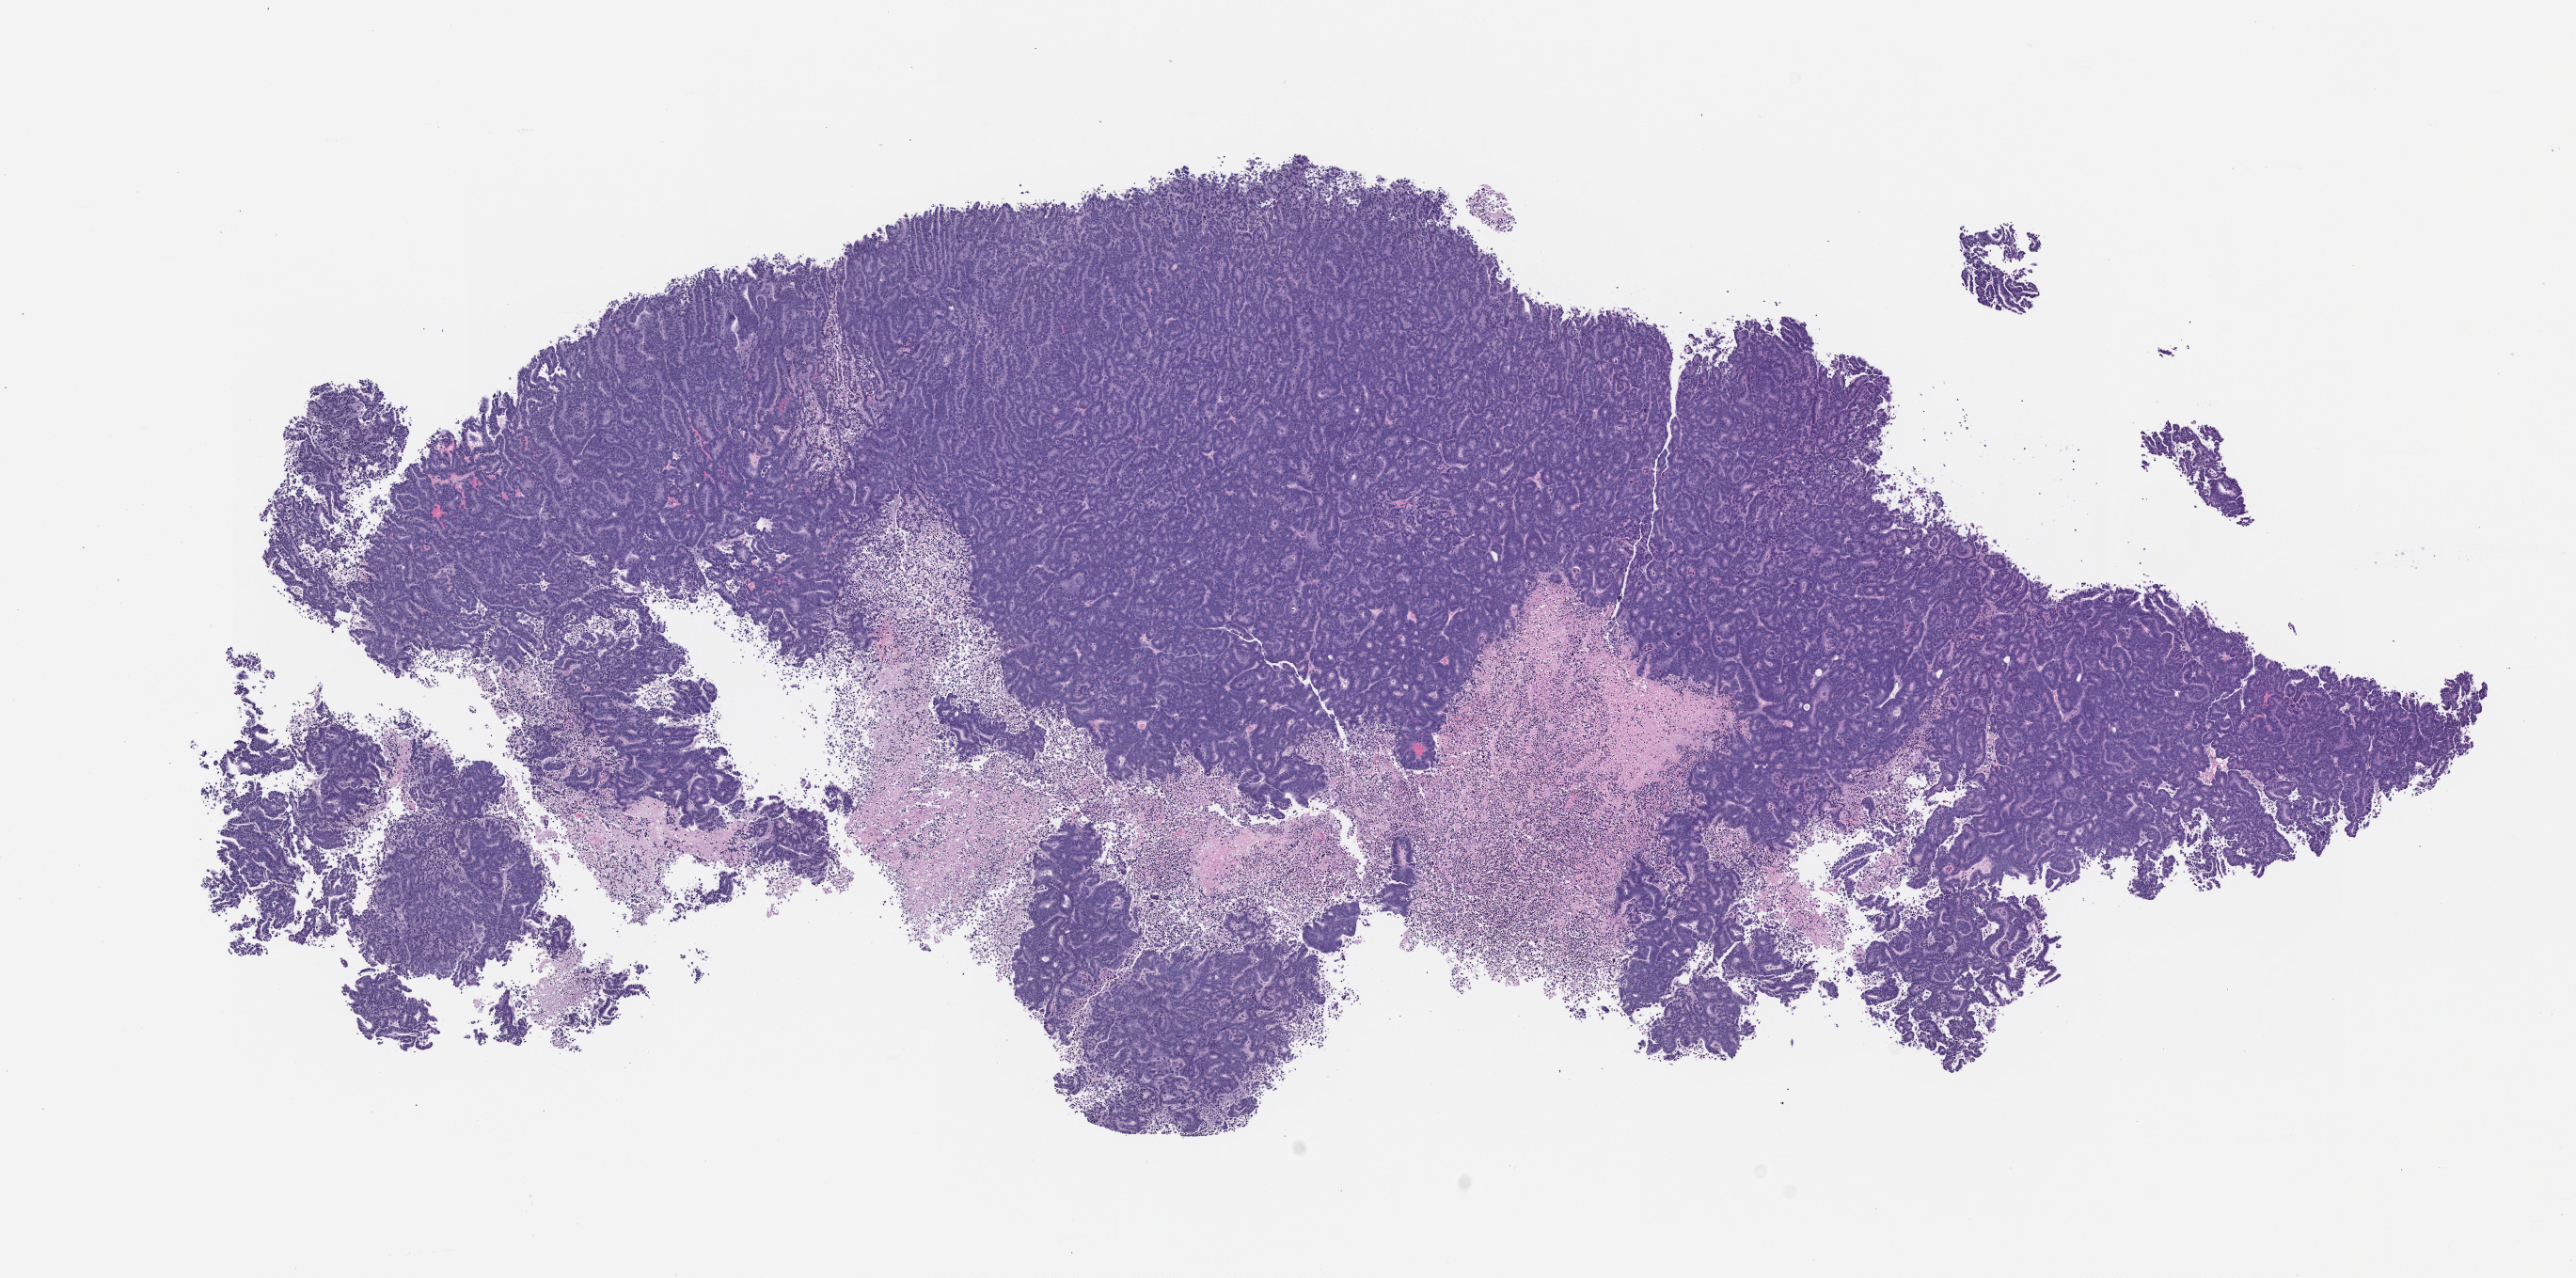
Hematoxylin and eosin (H&E) whole-slide image of a patient-derived xenograft (PDX) tumor grown in a mouse — whole scanned area (about 11.0 x 5.5 mm) shown as a low-resolution overview, FFPE section, tumor site category: small intestine.
- originating patient diagnosis: Small Intestinal Adenocarcinoma